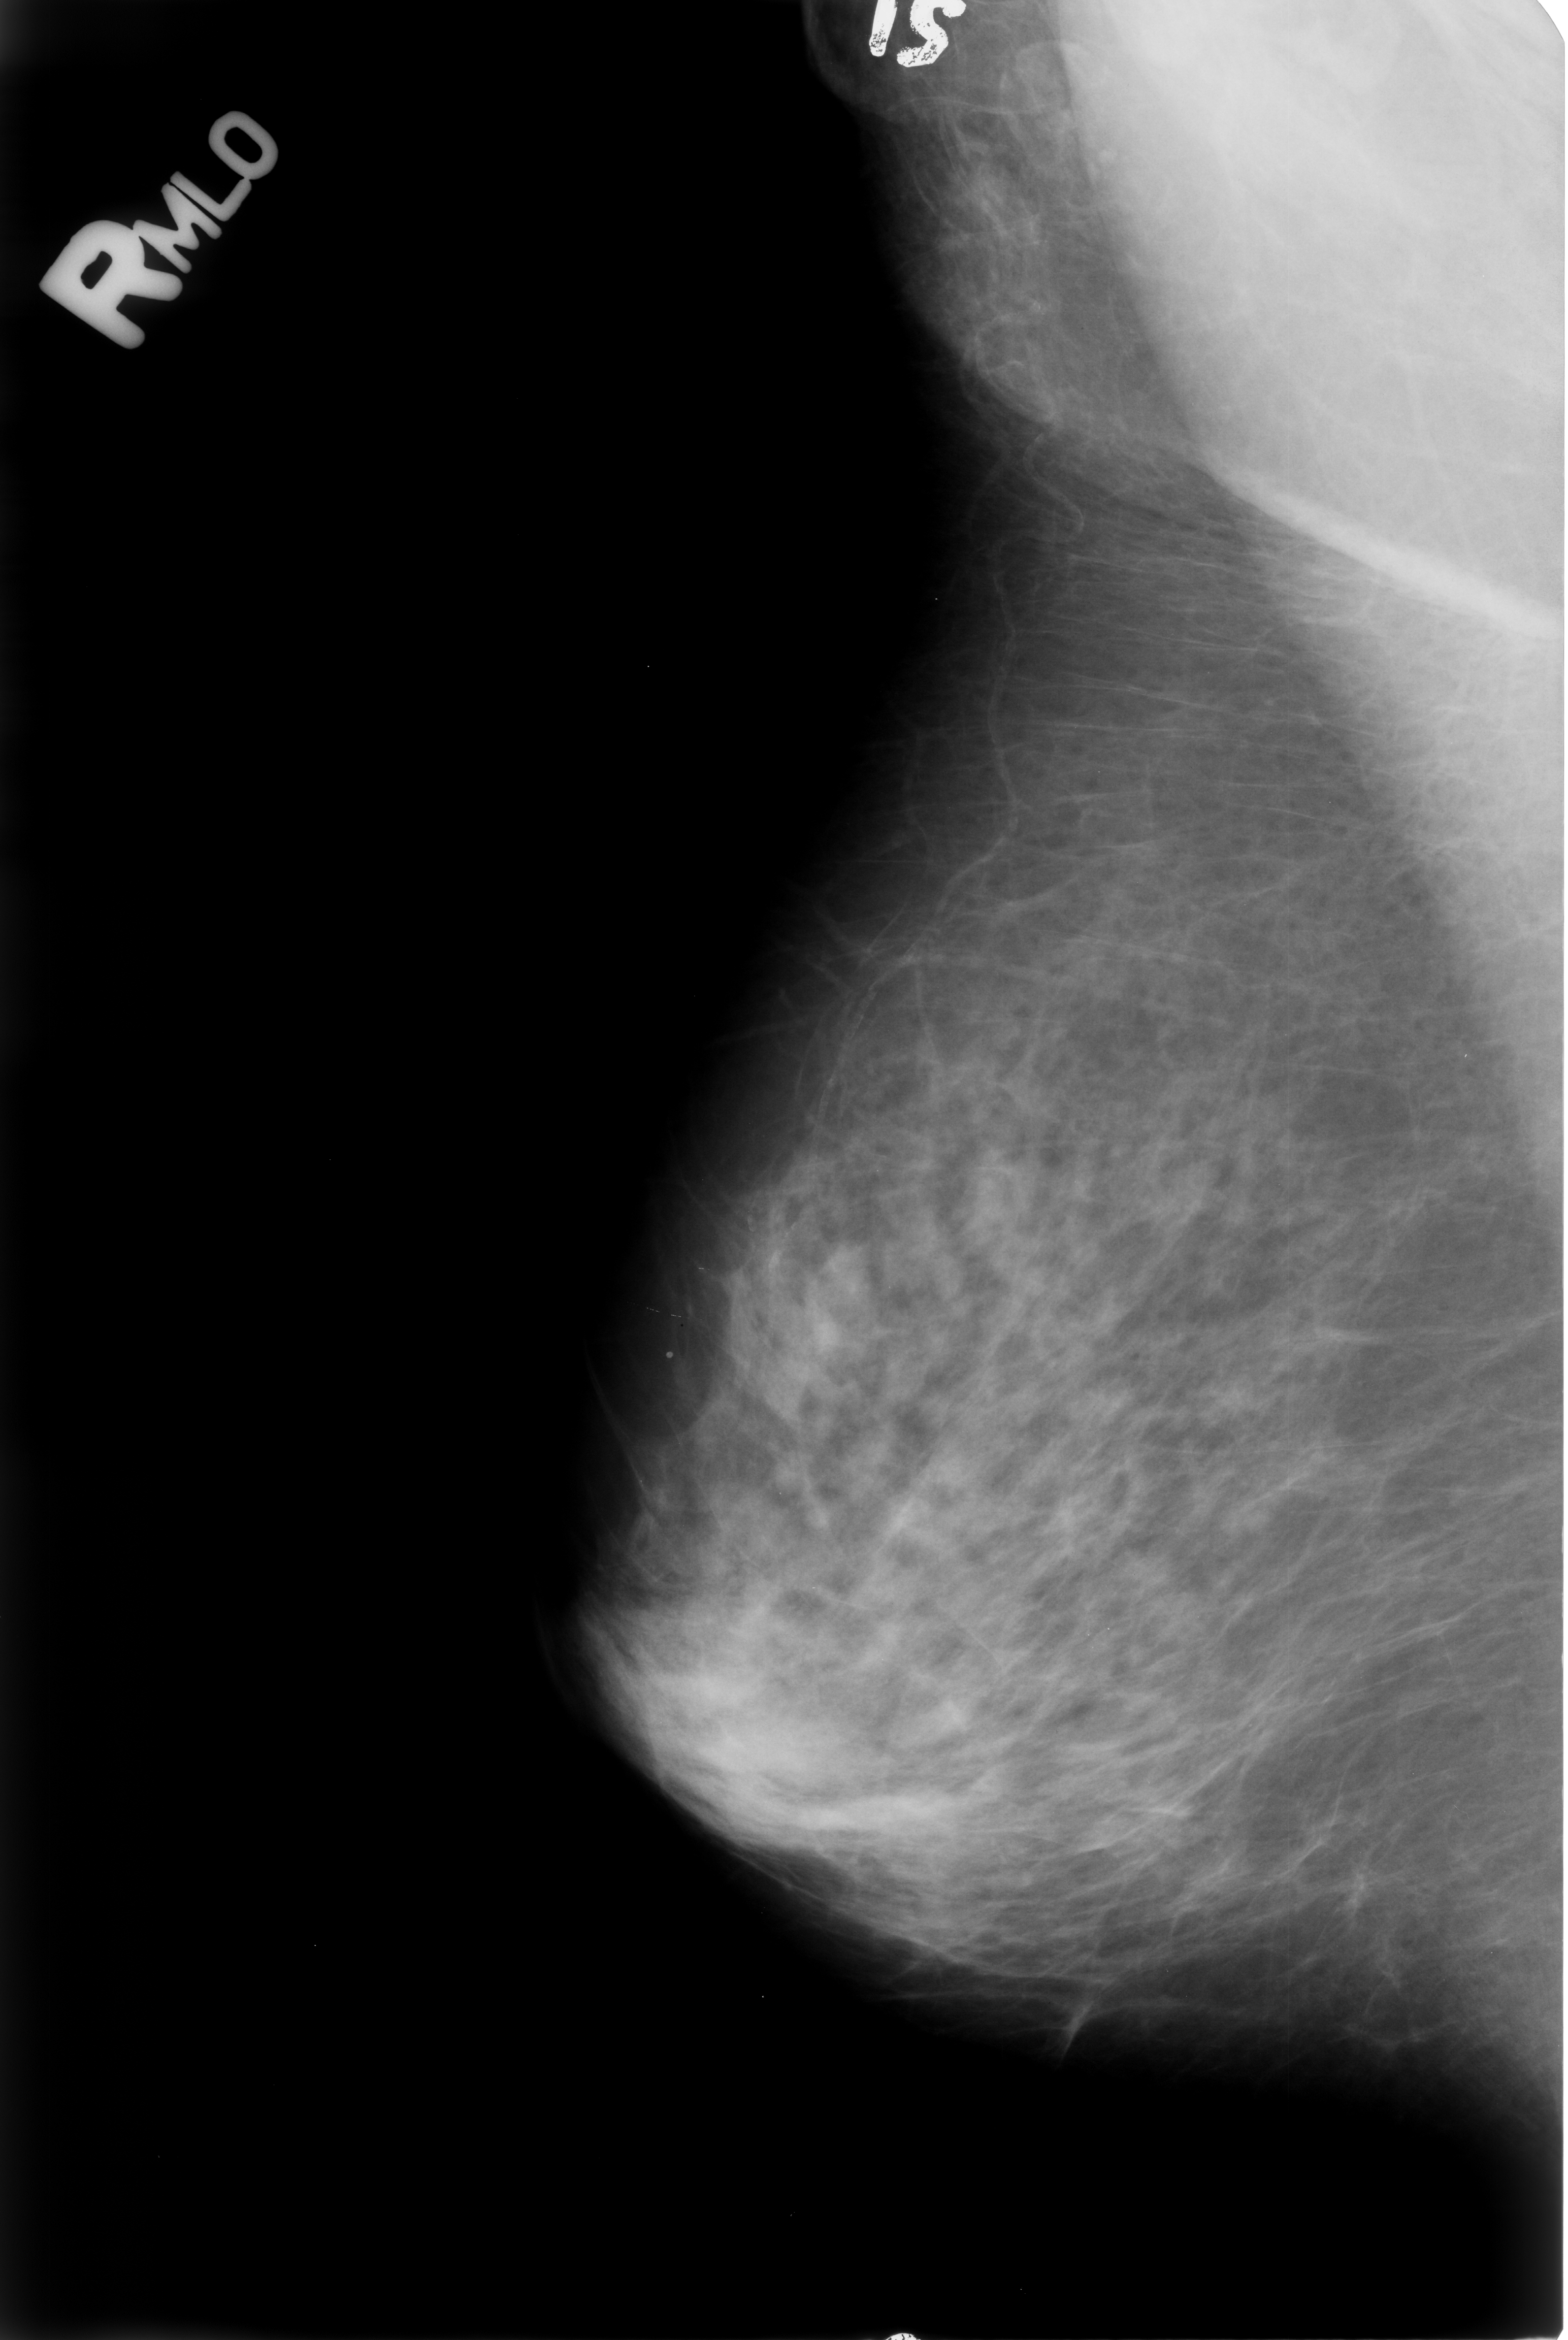
Digitized screen-film mammogram, right breast, MLO view, breast composition: heterogeneously dense (BI-RADS density category 3 of 4).
Abnormality record for this image: Finding 1 of 2: calcifications, morphology vascular; BI-RADS assessment category 2; benign without callback (not worked up further). Finding 2 of 2: calcifications, morphology lucent center; BI-RADS assessment category 2; benign; no additional work-up was recommended (benign without callback).